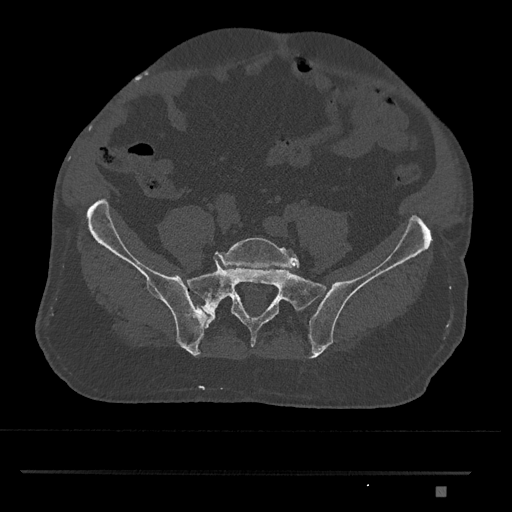
CT including the spine, one axial slice; position 517 of 1134 along the scan axis; reconstruction kernel Br40s/3; bone window (W 1800 / L 400 HU); 512 × 512 image matrix, field of view 429 × 429 mm. Patient: male, 65 years. Case-level facts recorded for this patient, not image findings: primary cancer: prostate.
Outlined on this slice (semi-automatically segmented with operator editing):
- L5 vertebra: bounding box <215,237,300,269> (left, top, right, bottom; pixels)